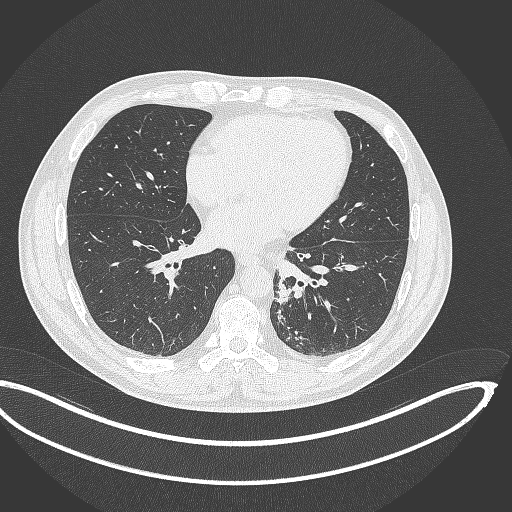
Chest CT, one axial slice; position 140 of 362 along the scan axis; reconstruction kernel B70f; 120 kVp; lung window (W 1500 / L -600 HU); 512 × 512 image matrix, field of view 442 × 442 mm. Patient: male, 50 years. From the clinical record (not read from this slice): clinical TNM (as recorded): T2a N3 M0.
Annotated regions visible in this slice (rectangle marked by the reading radiologist):
- lung tumour (recorded histology: squamous cell carcinoma): bounding box (x1, y1, x2, y2) in pixels: (274, 276, 292, 307)